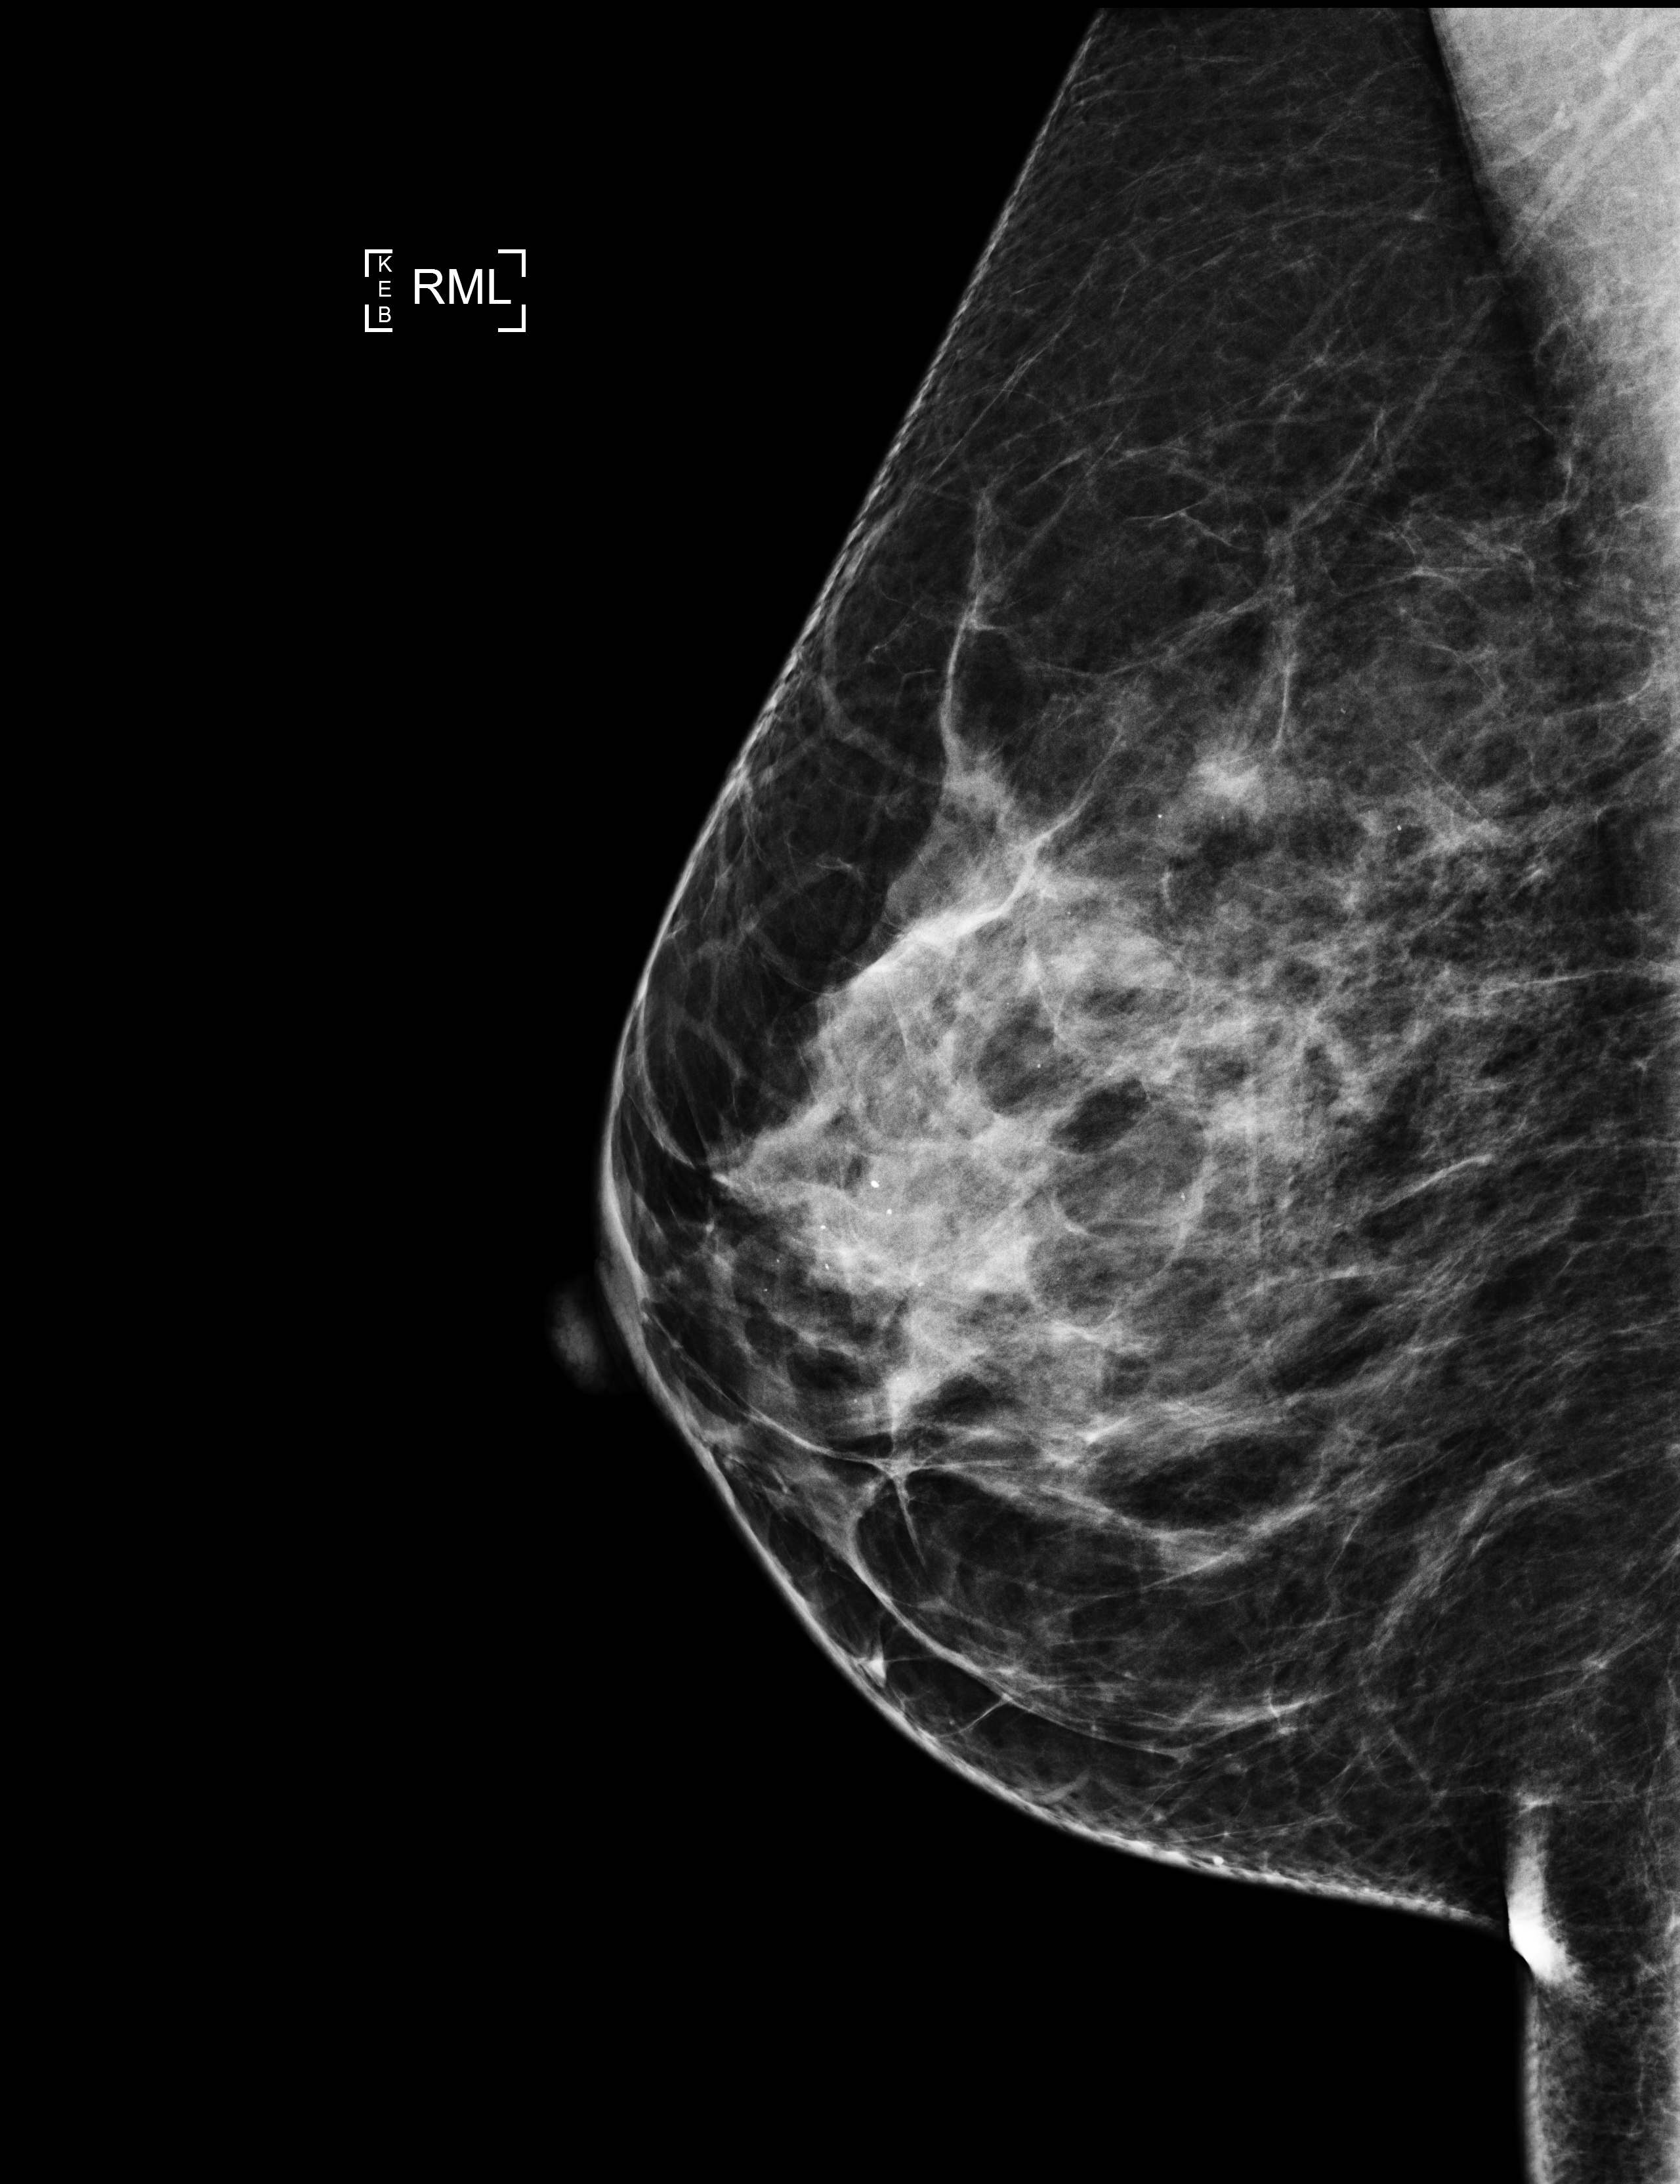
Digital mammogram (FFDM), right breast, ML view, diagnostic work-up study, compressed breast thickness 56 mm. Patient aged 41 years (female).
- breast density at the screening exam (both breasts): heterogeneously dense (BI-RADS density category c)
- final BI-RADS assessment for this screening round (tomosynthesis exam, both breasts): category 3
- recall: recalled for additional imaging after this screen